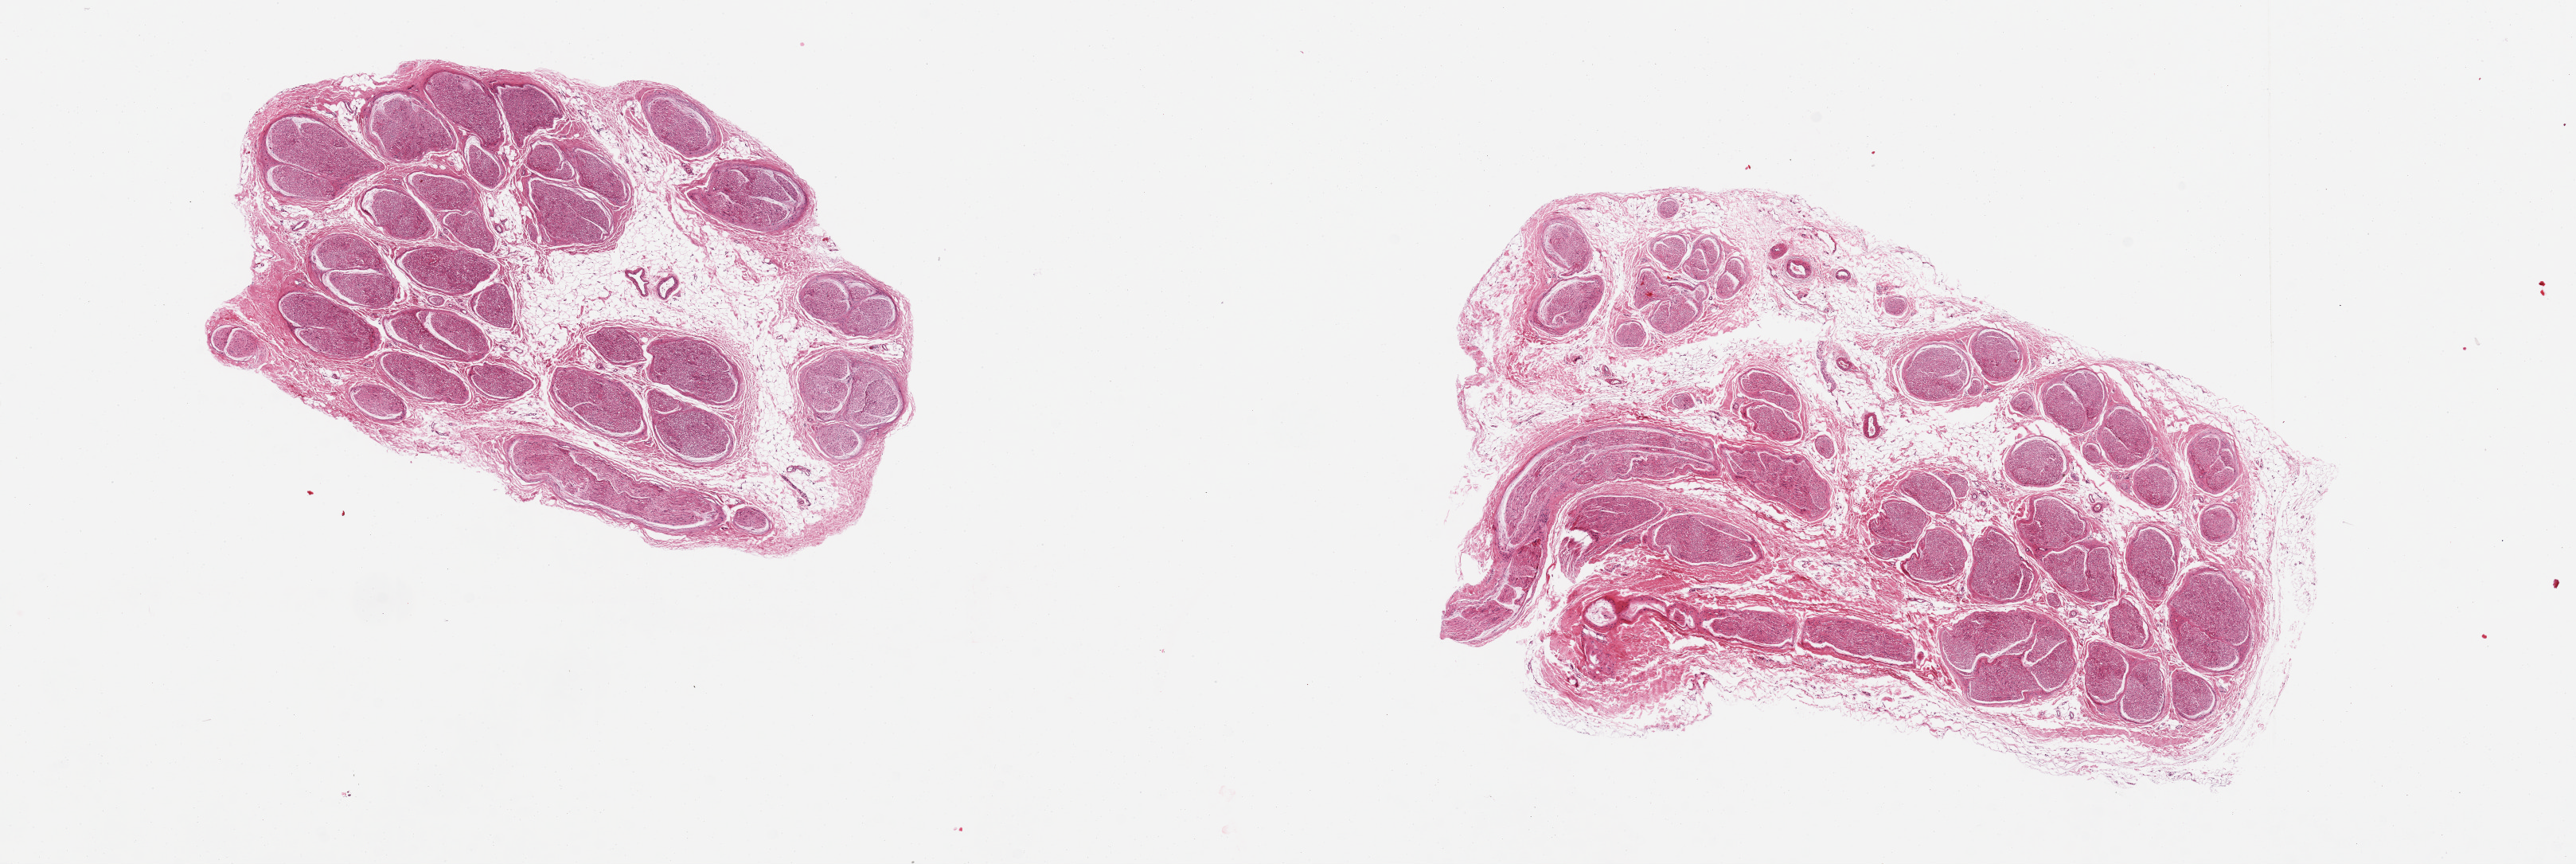
Digitized haematoxylin and eosin-stained section, shown as a low-resolution overview of the whole scanned area (about 25.6 x 8.6 mm), PAXgene-fixed, paraffin-embedded tissue, section of tibial nerve (target tissue), tissue donor sample. Female donor.
Review note (as recorded): 2 pieces, clean specimens; moderate interstitial adipose tissue.